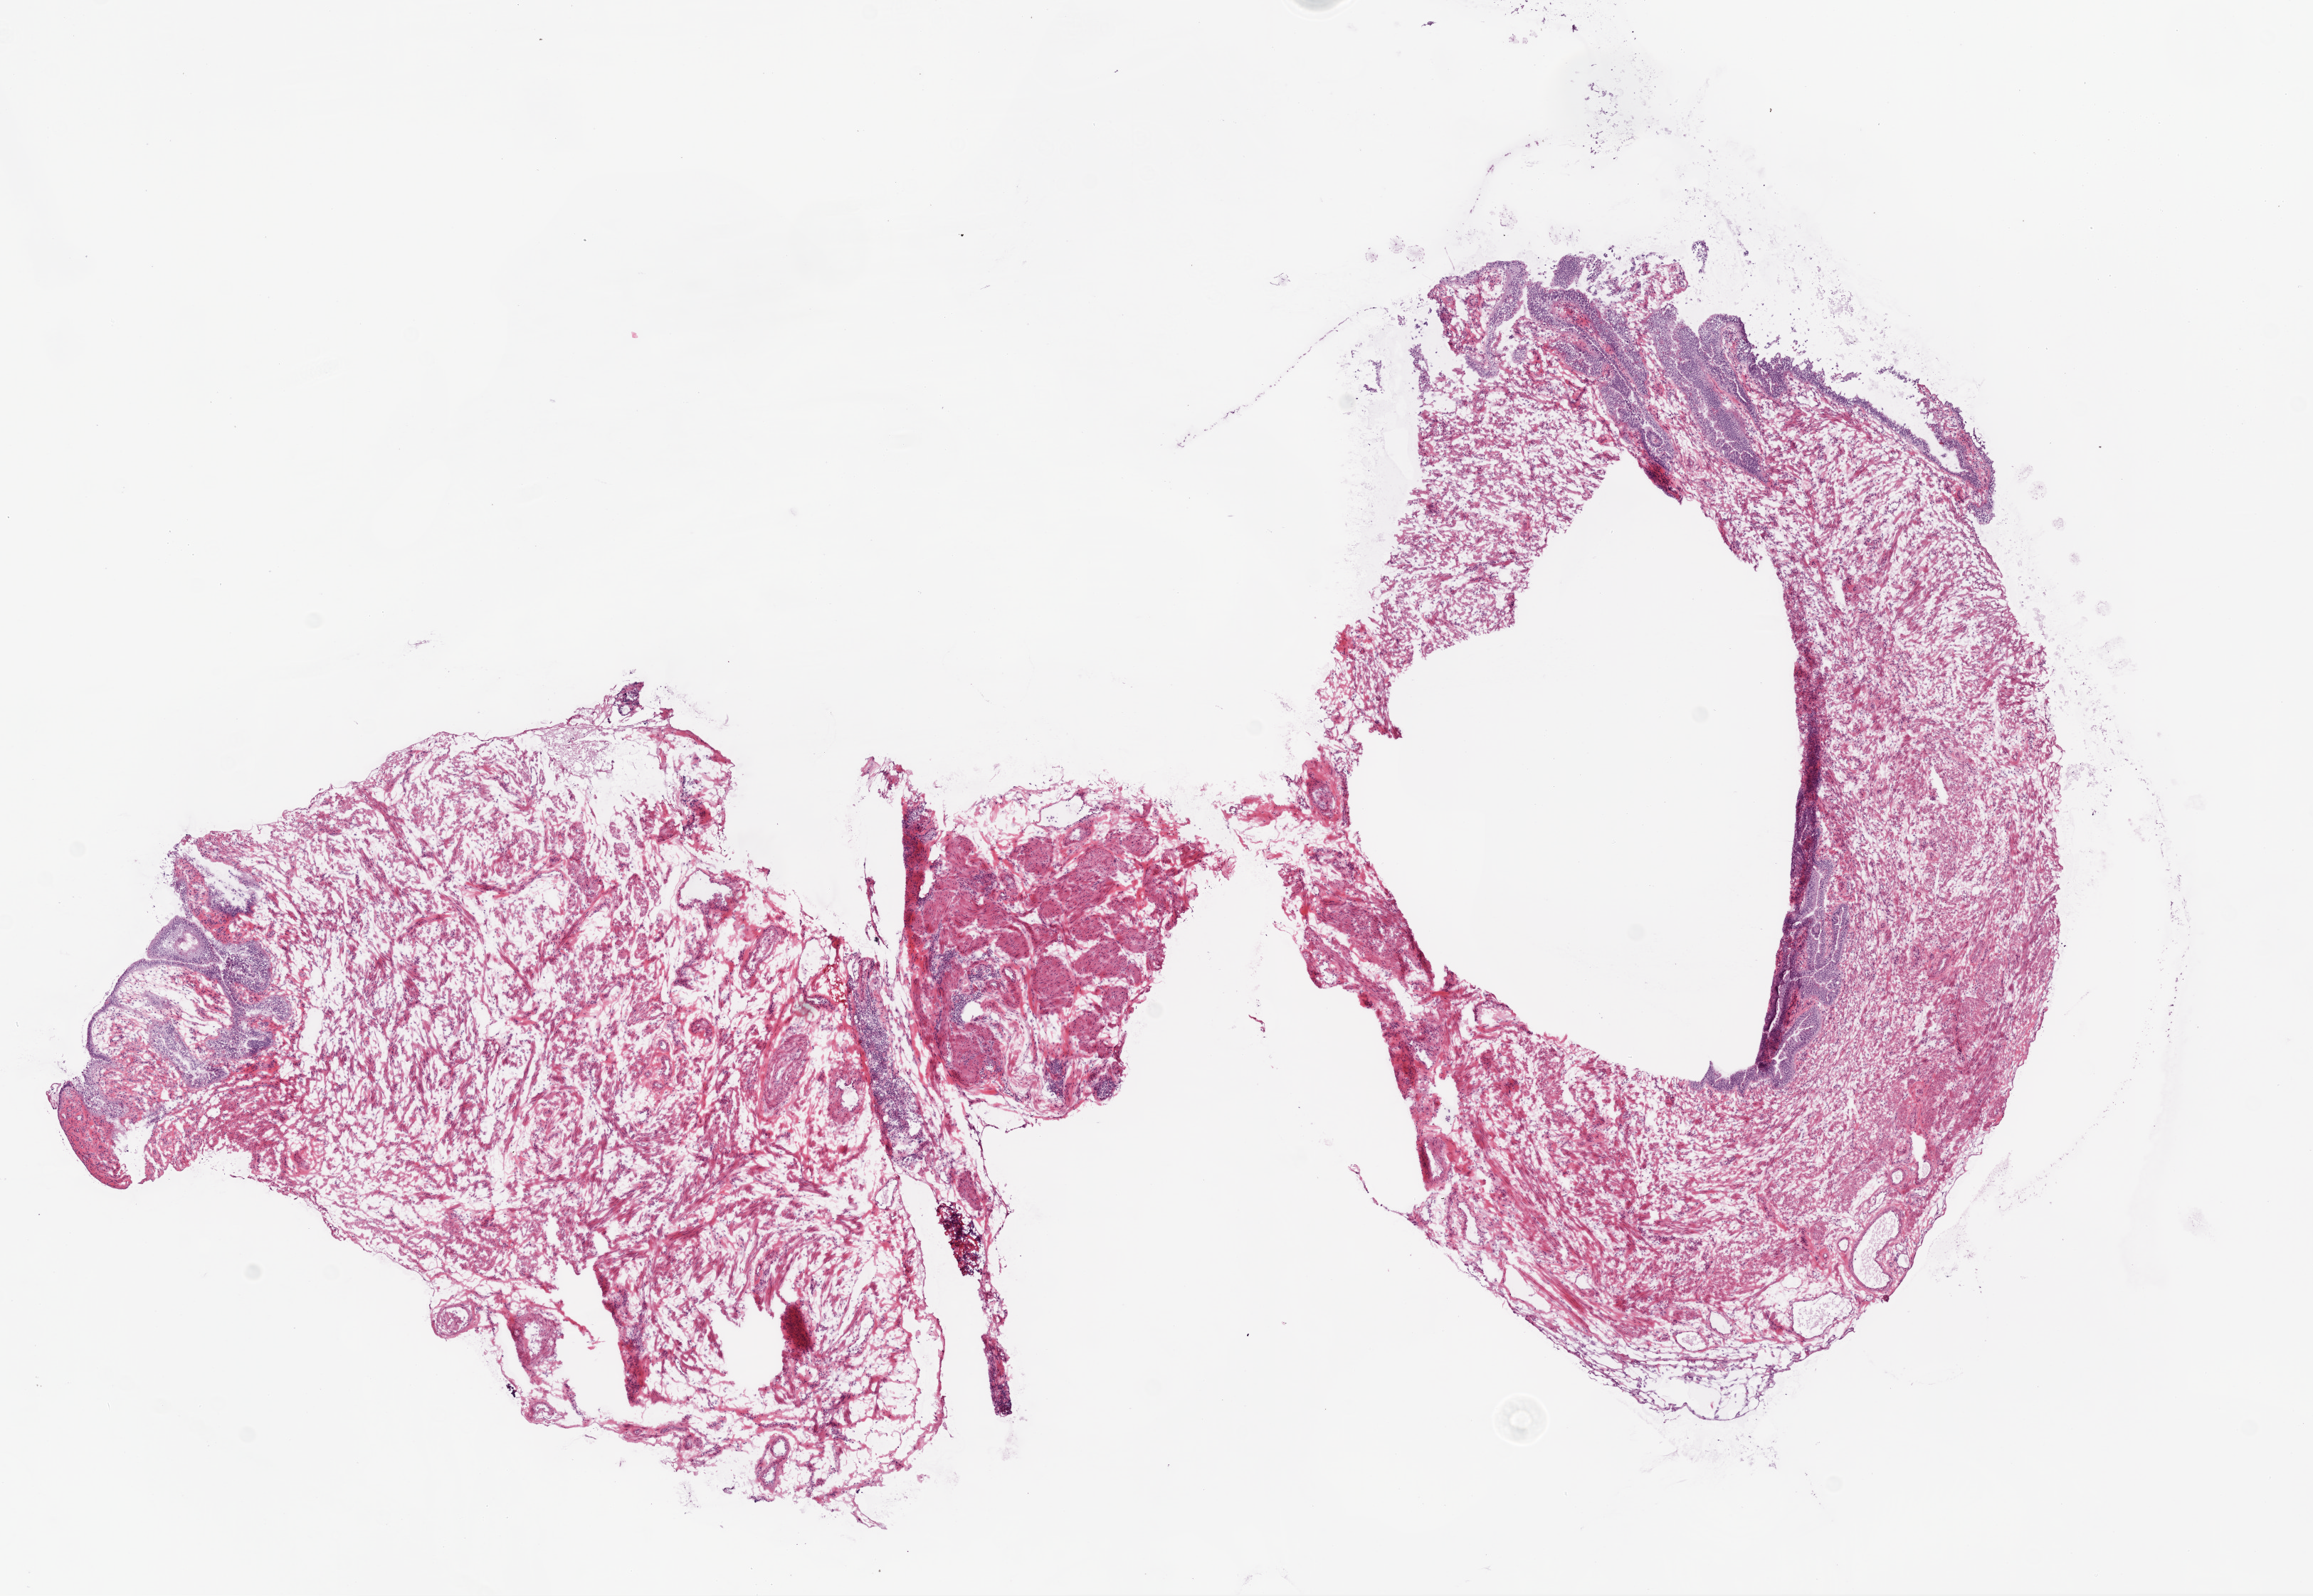
Whole-slide histology image, H&E, a low-resolution overview of the entire scanned area, about 13.0 x 9.0 mm (acquisition: 20x scan); frozen section from the bottom of the tissue portion; ovary, solid tissue normal (non-tumour tissue) sample. Patient: female, age at initial diagnosis 51 years.
This section: solid tissue normal sample (biorepository sample class). Patient diagnosis: Serous cystadenocarcinoma, NOS.